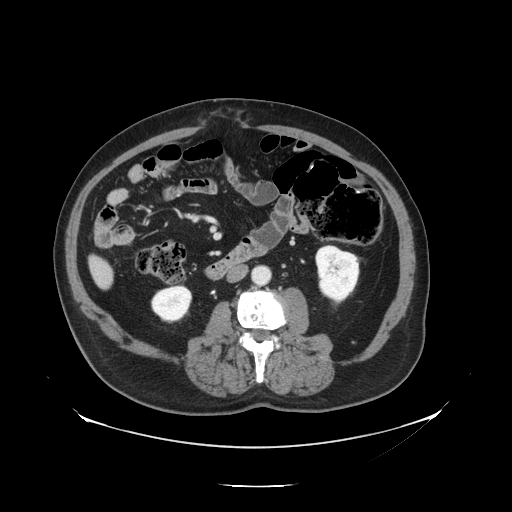
Contrast-enhanced abdominal CT, one axial slice; position 33 of 138 along the scan axis; reconstruction kernel STANDARD; 120 kVp; intravenous contrast given; soft-tissue window (W 400 / L 40 HU); 2.5 mm slice thickness; 512 × 512 image matrix, field of view 497 × 497 mm. Male patient, age 77 years. Case-level facts recorded for this patient, not image findings: diagnosis: colorectal cancer liver metastases, imaged before liver resection; multiple liver metastases: no; largest metastasis: 1.5 cm; disease in both lobes: no.
Outlined on this slice (outlined manually by an expert reader):
- liver: box from (x=92, y=259) to (x=113, y=287) px
- planned liver remnant (the part of the liver to remain after resection): (x=91, y=258)–(x=109, y=274)